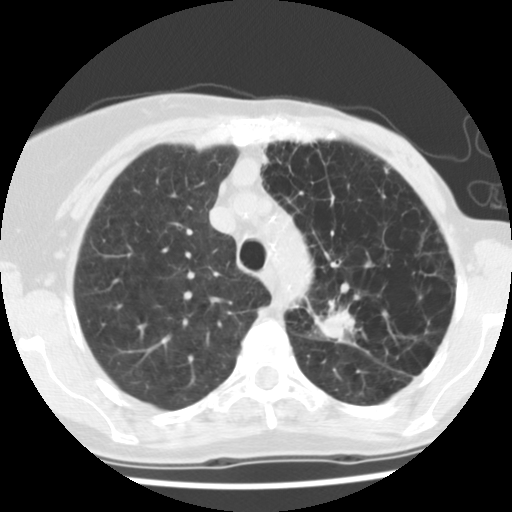
Chest CT (low-dose screening protocol), one axial image; first (baseline) screen; lung window (W 1500 / L -600 HU); 2.5 mm slice thickness; slice 32 of 128 in the series. Female, age 67 years at enrolment. Current smoker at enrolment.
- Lesion marked by an expert reader, bounding box (x1, y1, x2, y2) in pixels: (301, 285, 381, 360).
- The screening reader recorded 2 non-calcified nodules or masses ≥4 mm on this exam (left upper lobe, left lower lobe); which of them this box marks is not recorded.
- Official screen result: positive, change unspecified: nodule(s) >= 4 mm or enlarging nodule(s), mass(es), or other non-specific abnormalities suspicious for lung cancer.
- Lung cancer was diagnosed 109 days after this screen: adenocarcinoma, NOS, left upper lobe, poorly differentiated (G3), stage IIB (AJCC 6th edition), 45 mm at pathology.